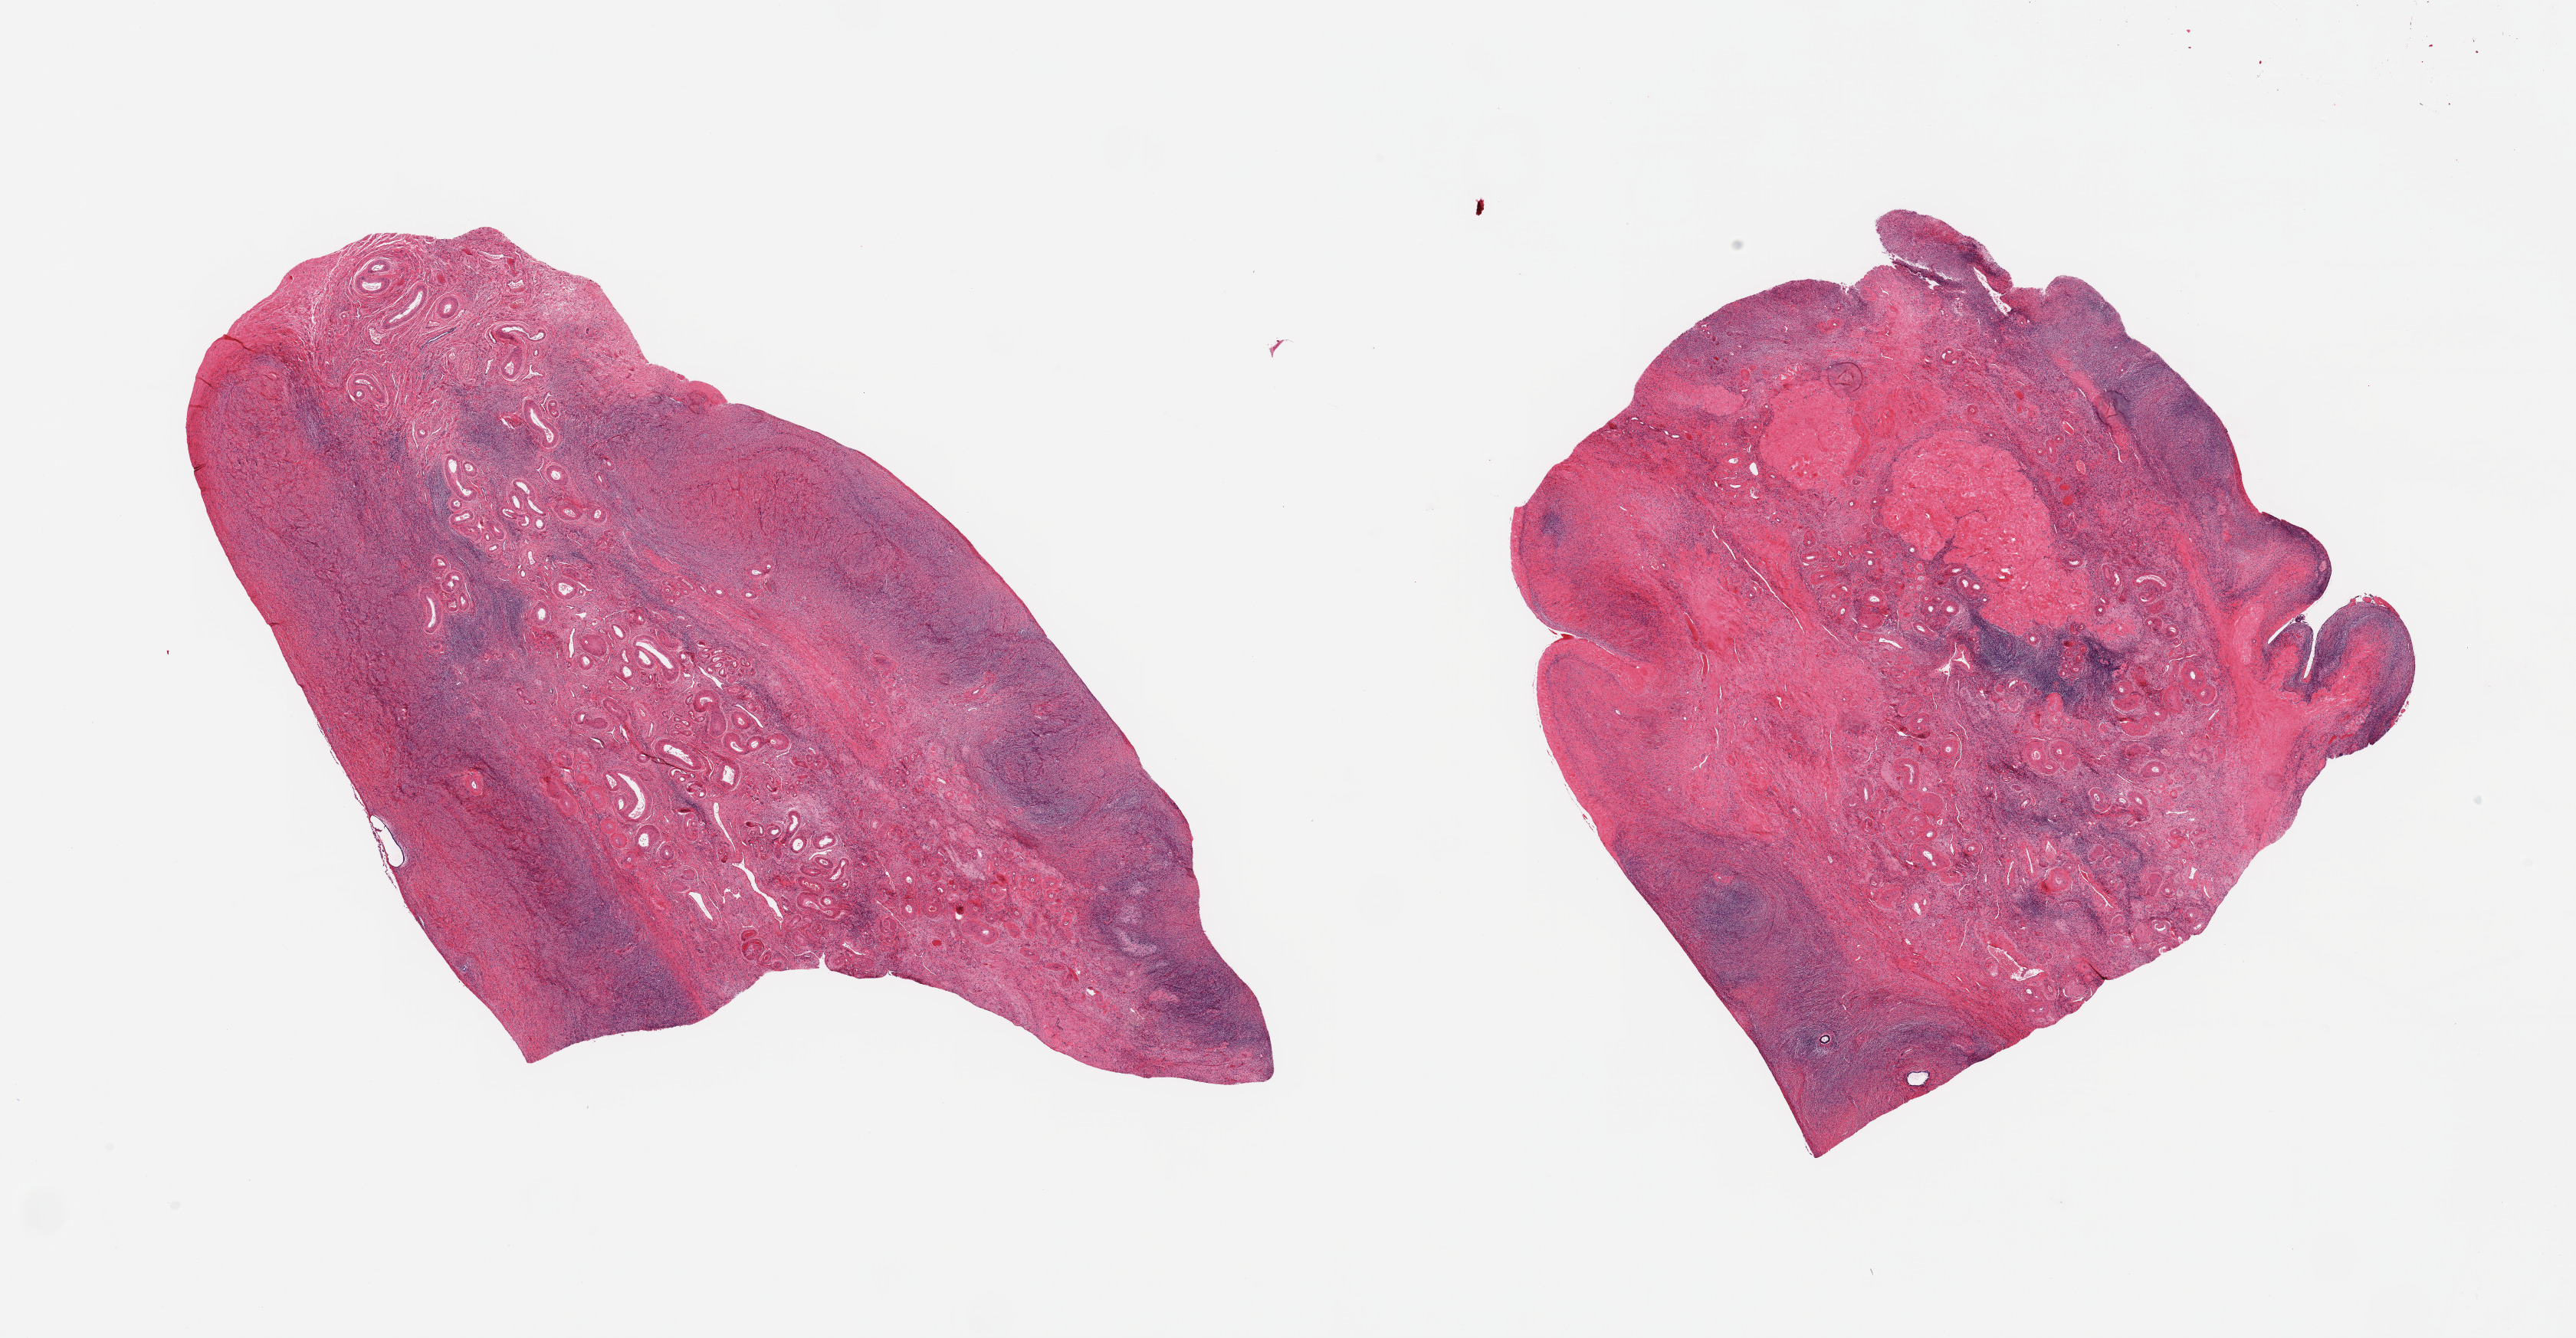
Whole-slide image, haematoxylin and eosin stain, a low-resolution overview of the entire scanned area, about 26.6 x 13.8 mm (slide scanned at 20x). PAXgene-fixed paraffin-embedded (PFPE) section. Sampled site (target tissue): ovary. Tissue donor sample. Donor sex: female.
Reviewer comment on this tissue sample: 2 pieces; atrophic with thin (1-1.6 mm) outer rim of parenchyma; inner core is largely fibrovascular and corpora albicantia.